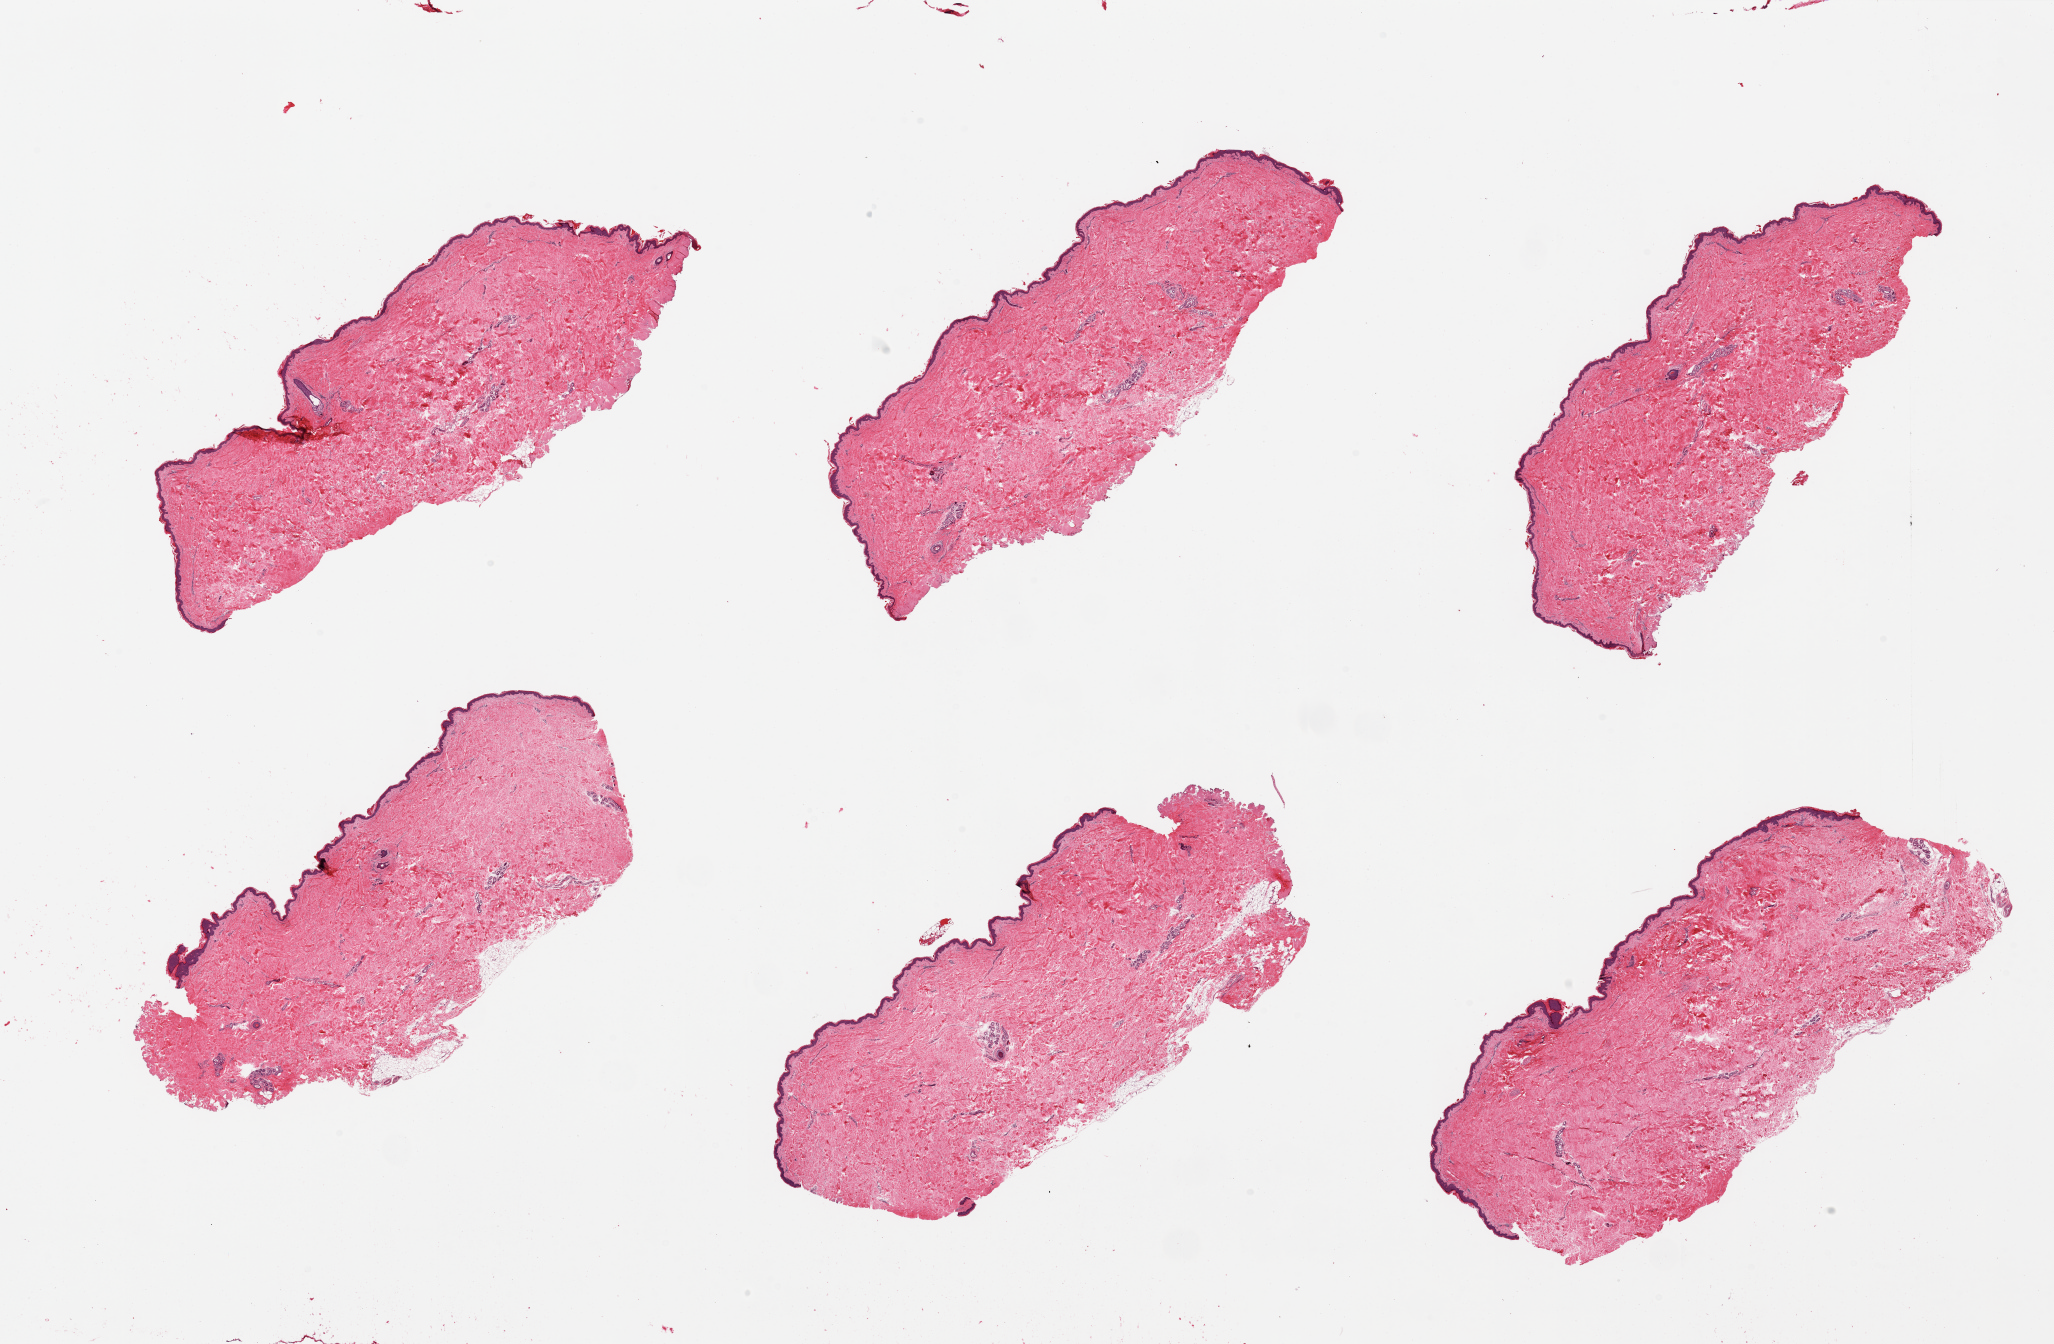
Digitized haematoxylin and eosin-stained section — low-resolution overview of the scanned area, about 32.5 x 21.3 mm, PAXgene-fixed paraffin-embedded (PFPE) section, target tissue: skin of suprapubic region, donor tissue sample. Female donor.
- reviewer comment on this tissue sample: 6 pieces. Squamous epithelium is 1.5-2% thickness